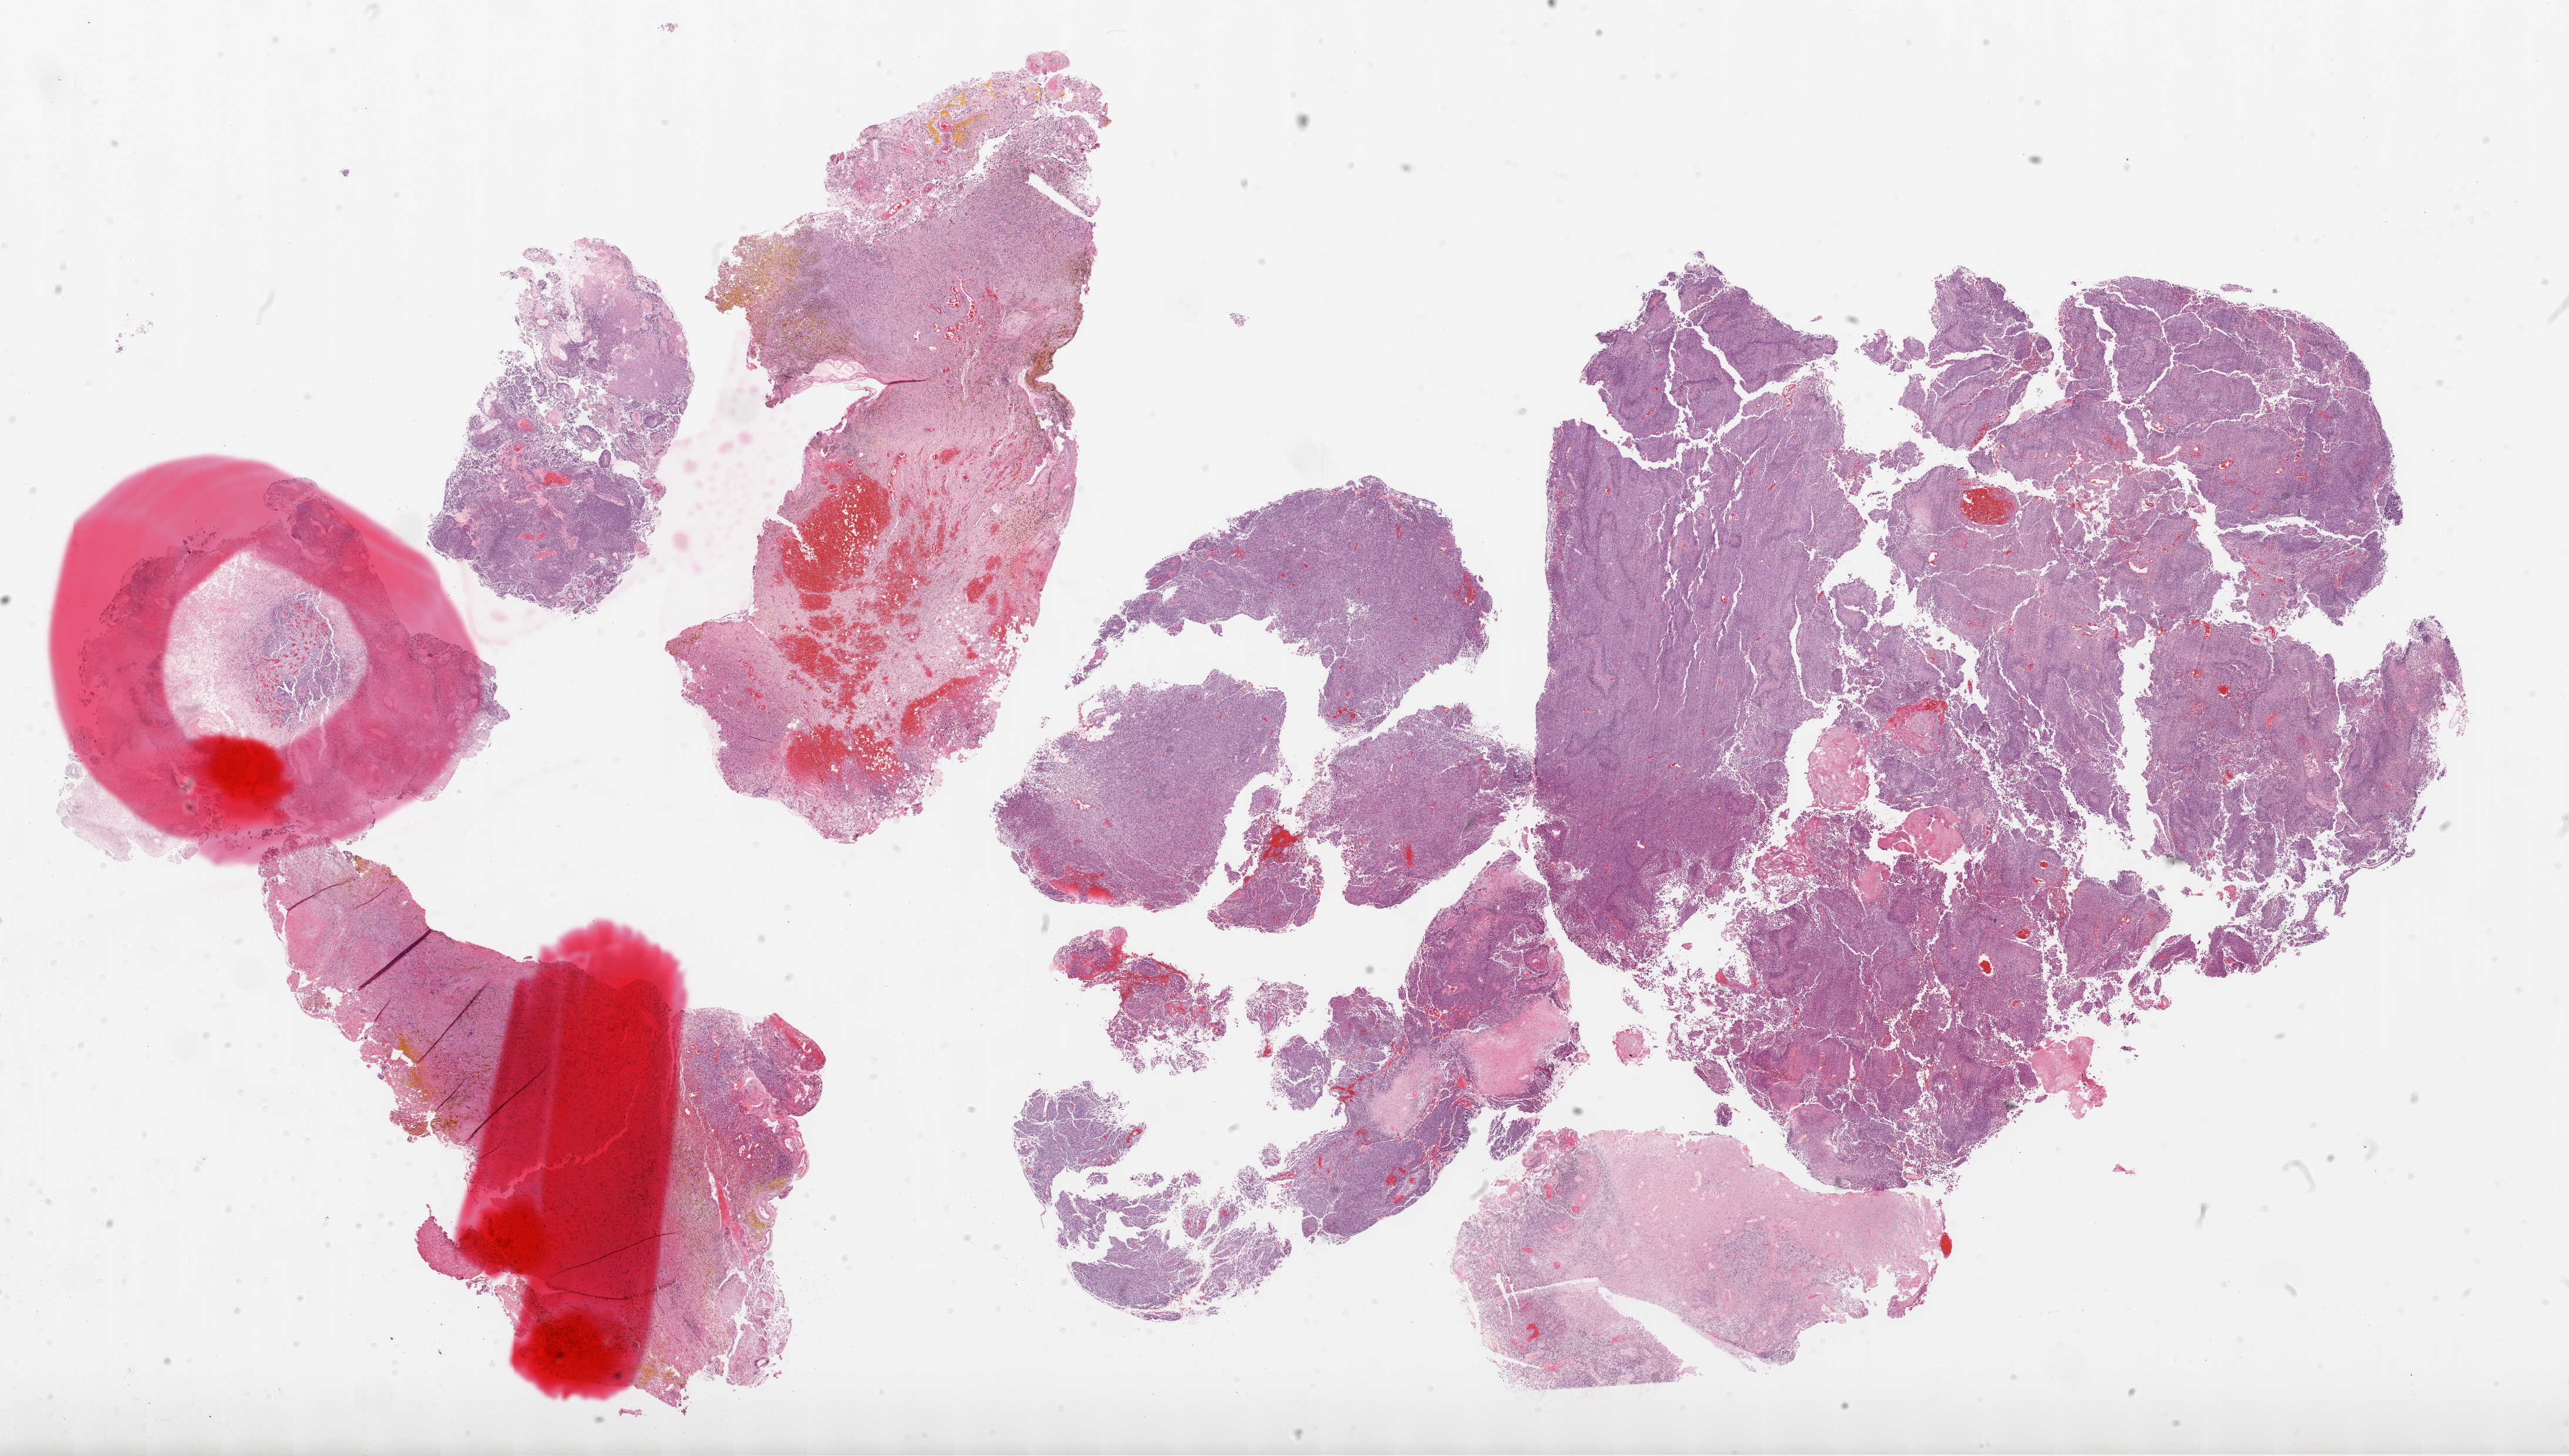
Whole-slide histology image, H&E-stained, shown as a low-resolution overview of the whole scanned area (about 35.1 x 19.9 mm, slide scanned at 20x), formalin-fixed paraffin-embedded (FFPE) diagnostic section, sample: primary tumour, brain. Patient: male, age at initial diagnosis 61 years.
Histologic diagnosis: Glioblastoma.